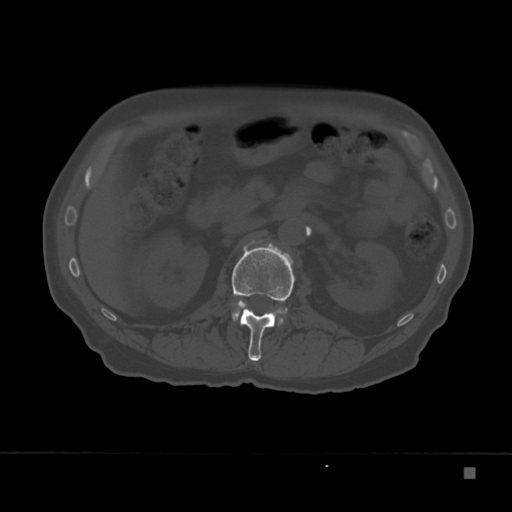
CT including the spine, one axial slice; position 106 of 332 along the scan axis; reconstruction kernel Br40s; 120 kVp; bone window (W 1800 / L 400 HU); 512 × 512 image matrix, field of view 389 × 389 mm. Male patient, age 72 years. From the clinical record (not read from this slice): primary cancer: skeletal.
Structures marked on this image (semi-automatic segmentation, software-assisted and operator-edited):
- L1 vertebra: bounding box <232,240,295,361> (left, top, right, bottom; pixels)
- L2 vertebra: <232,309,285,326>